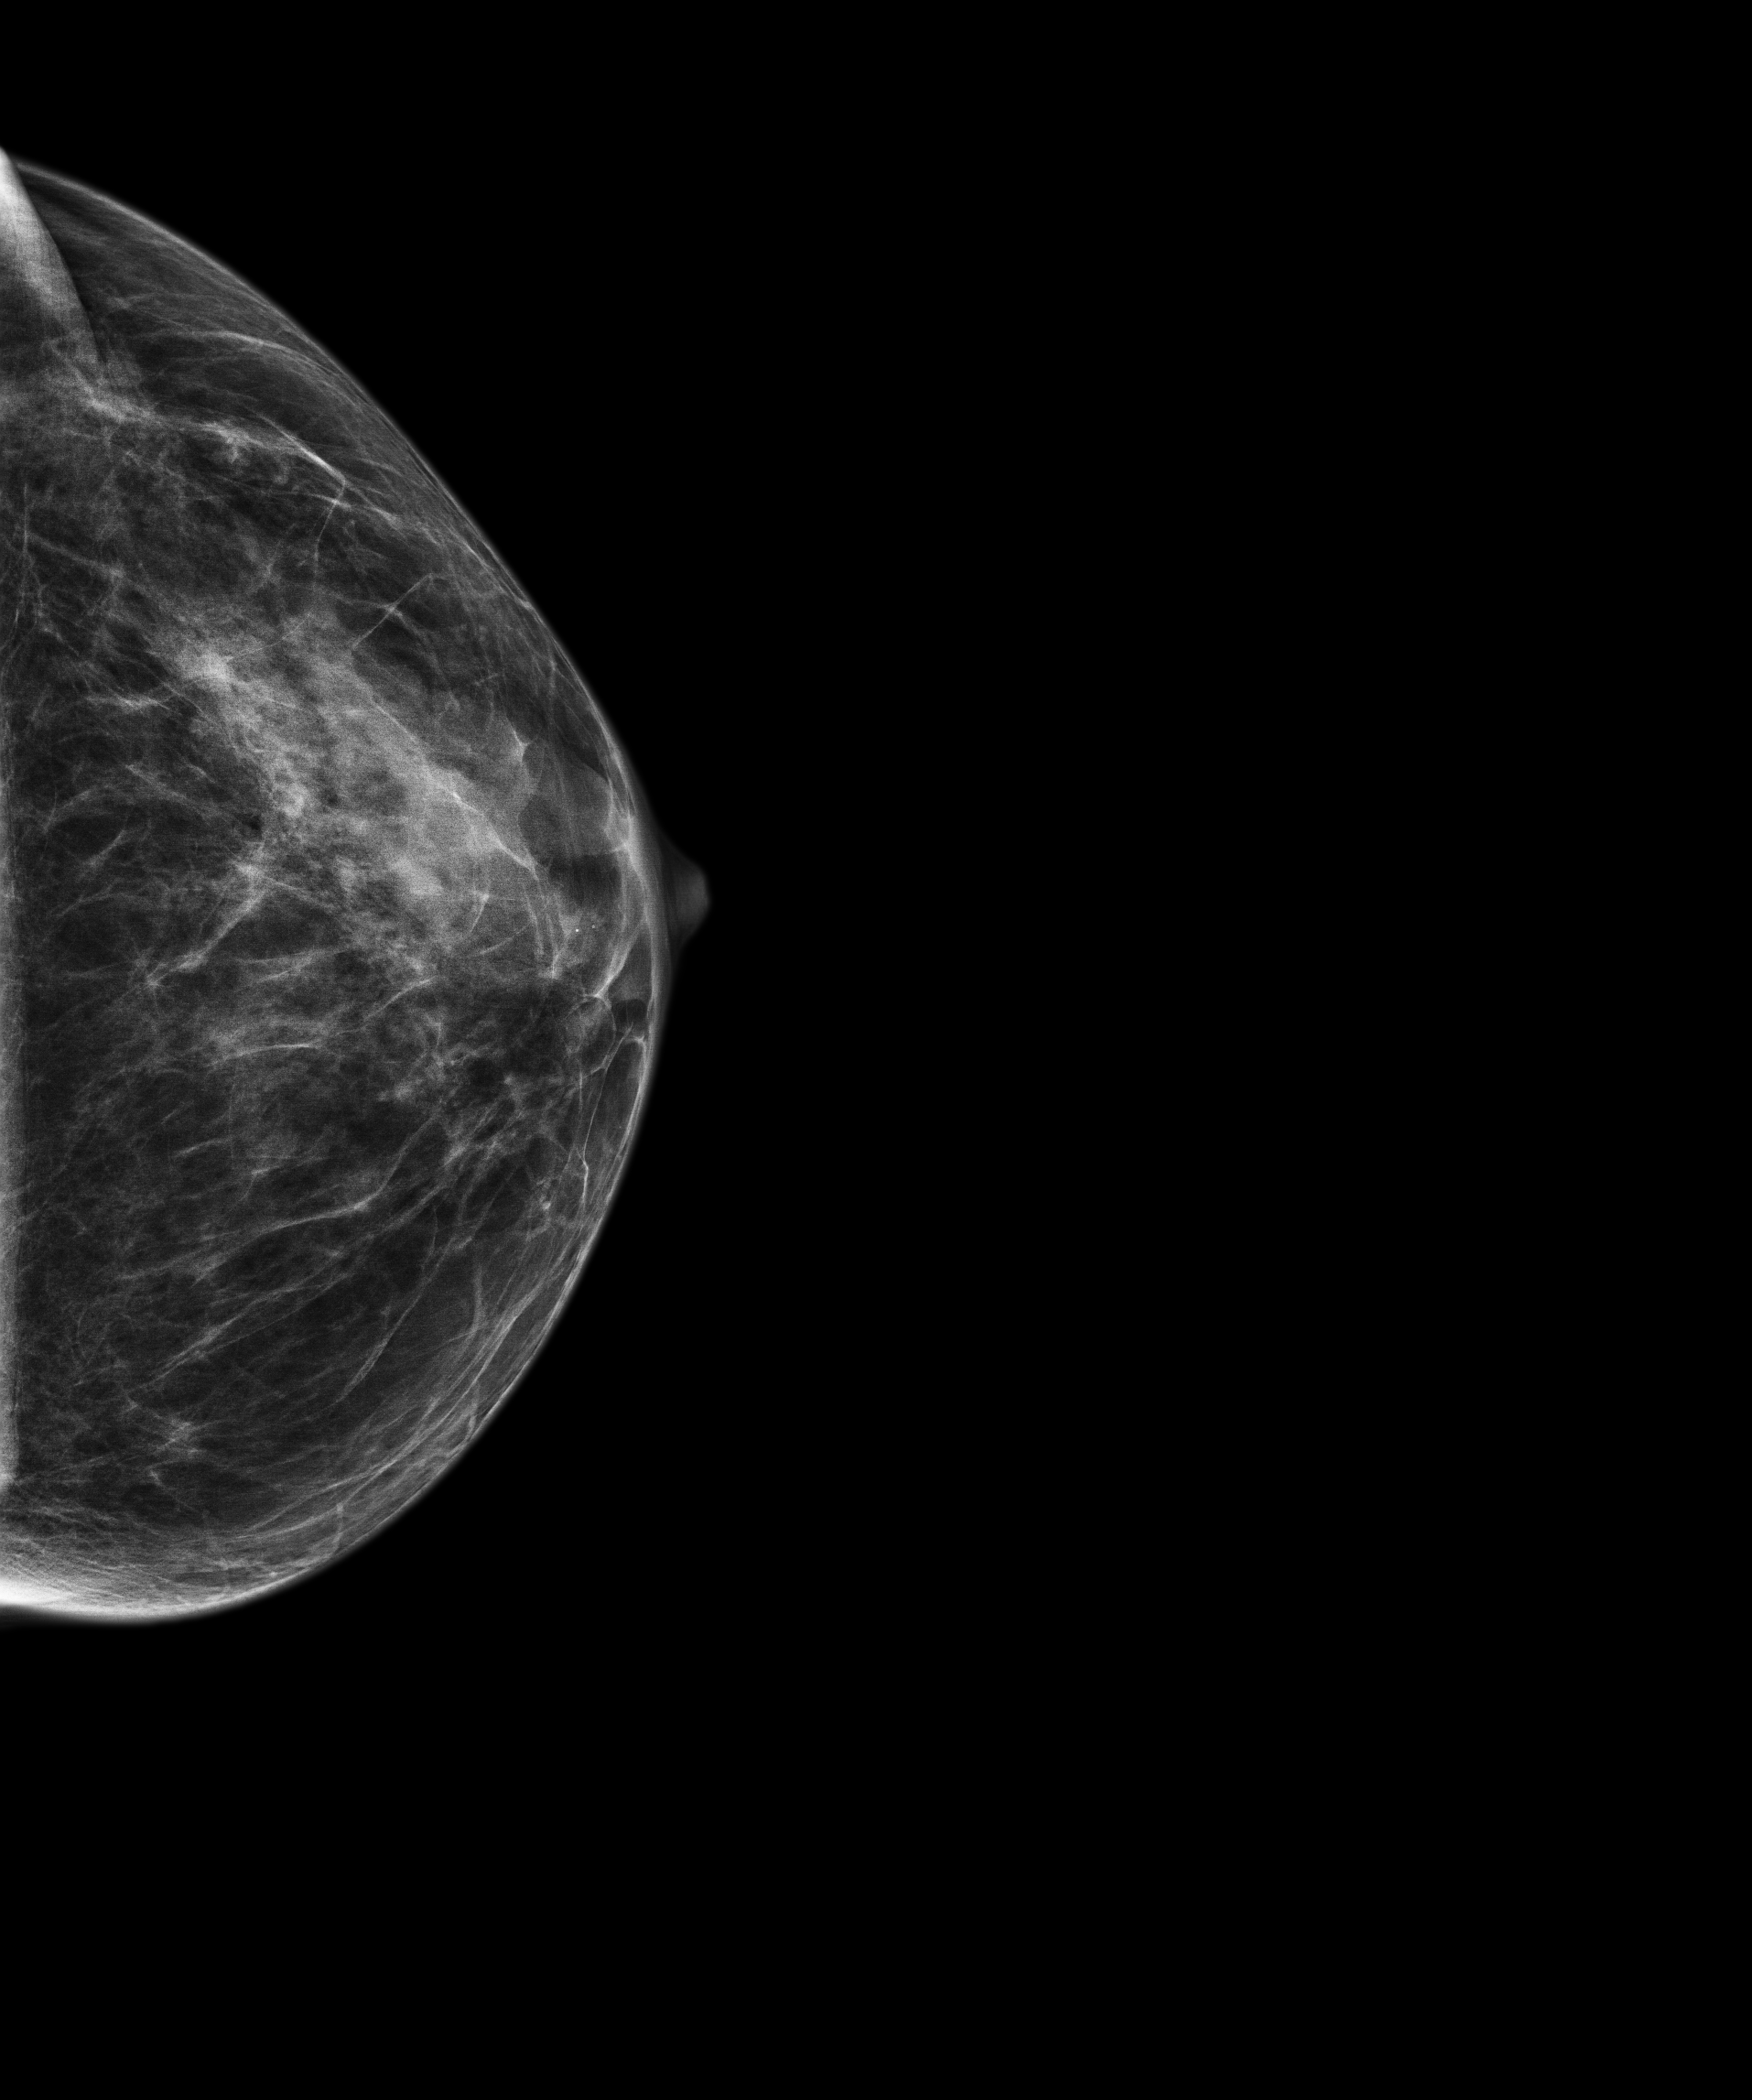
Annual screening mammography examination, system: Senographe Pristina. Patient aged 66 years (female).
Image type: full-field digital mammogram. Breast: left. Projection: CC view.